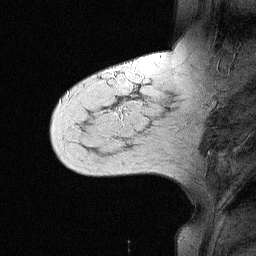
Breast MRI (dynamic contrast-enhanced), one sagittal slice. Dynamic contrast-enhanced study with each time point stored as its own series, time point 2 of 3 at this slice position (early post-contrast, ordered by acquisition time). 1.5 T. TE 4.5 ms, TR 11 ms. 256 × 256 image matrix. Female patient, age 55 years. From the clinical record (not read from this slice): setting: breast cancer imaged before/during neoadjuvant chemotherapy; receptor status: triple-negative.
Annotated regions visible in this slice (semi-automatic segmentation, software-assisted and operator-edited):
- analysis volume of interest (the breast-tissue region the enhancement analysis was run in; not a lesion): bounding box <71,63,147,145> (left, top, right, bottom; pixels)
- tumour enhancement mask (voxels above the 90 % enhancement threshold inside the analysis volume of interest): <112,111,121,113>